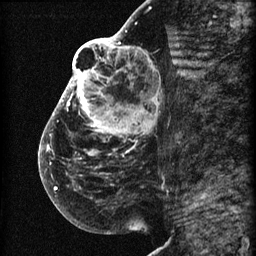
Breast MRI (dynamic contrast-enhanced), one sagittal slice; position 34 of 60 along the scan axis; 3 images stored at this slice position (order not interpretable as contrast timing); 1.5 T; TE 4.2 ms, TR 22.7 ms; 2 mm slice thickness; 256 × 256 image matrix, field of view 180 × 180 mm. Patient: female, 48 years. Case-level facts recorded for this patient, not image findings: setting: breast cancer imaged before/during neoadjuvant chemotherapy; receptor status: triple-negative.
Structures marked on this image (semi-automatically segmented with operator editing):
- analysis volume of interest (the breast-tissue region the enhancement analysis was run in; not a lesion): bounding box [x1, y1, x2, y2] px = [44, 30, 173, 207]
- tumour enhancement mask (voxels above the 90 % enhancement threshold inside the analysis volume of interest): [44, 30, 155, 190]